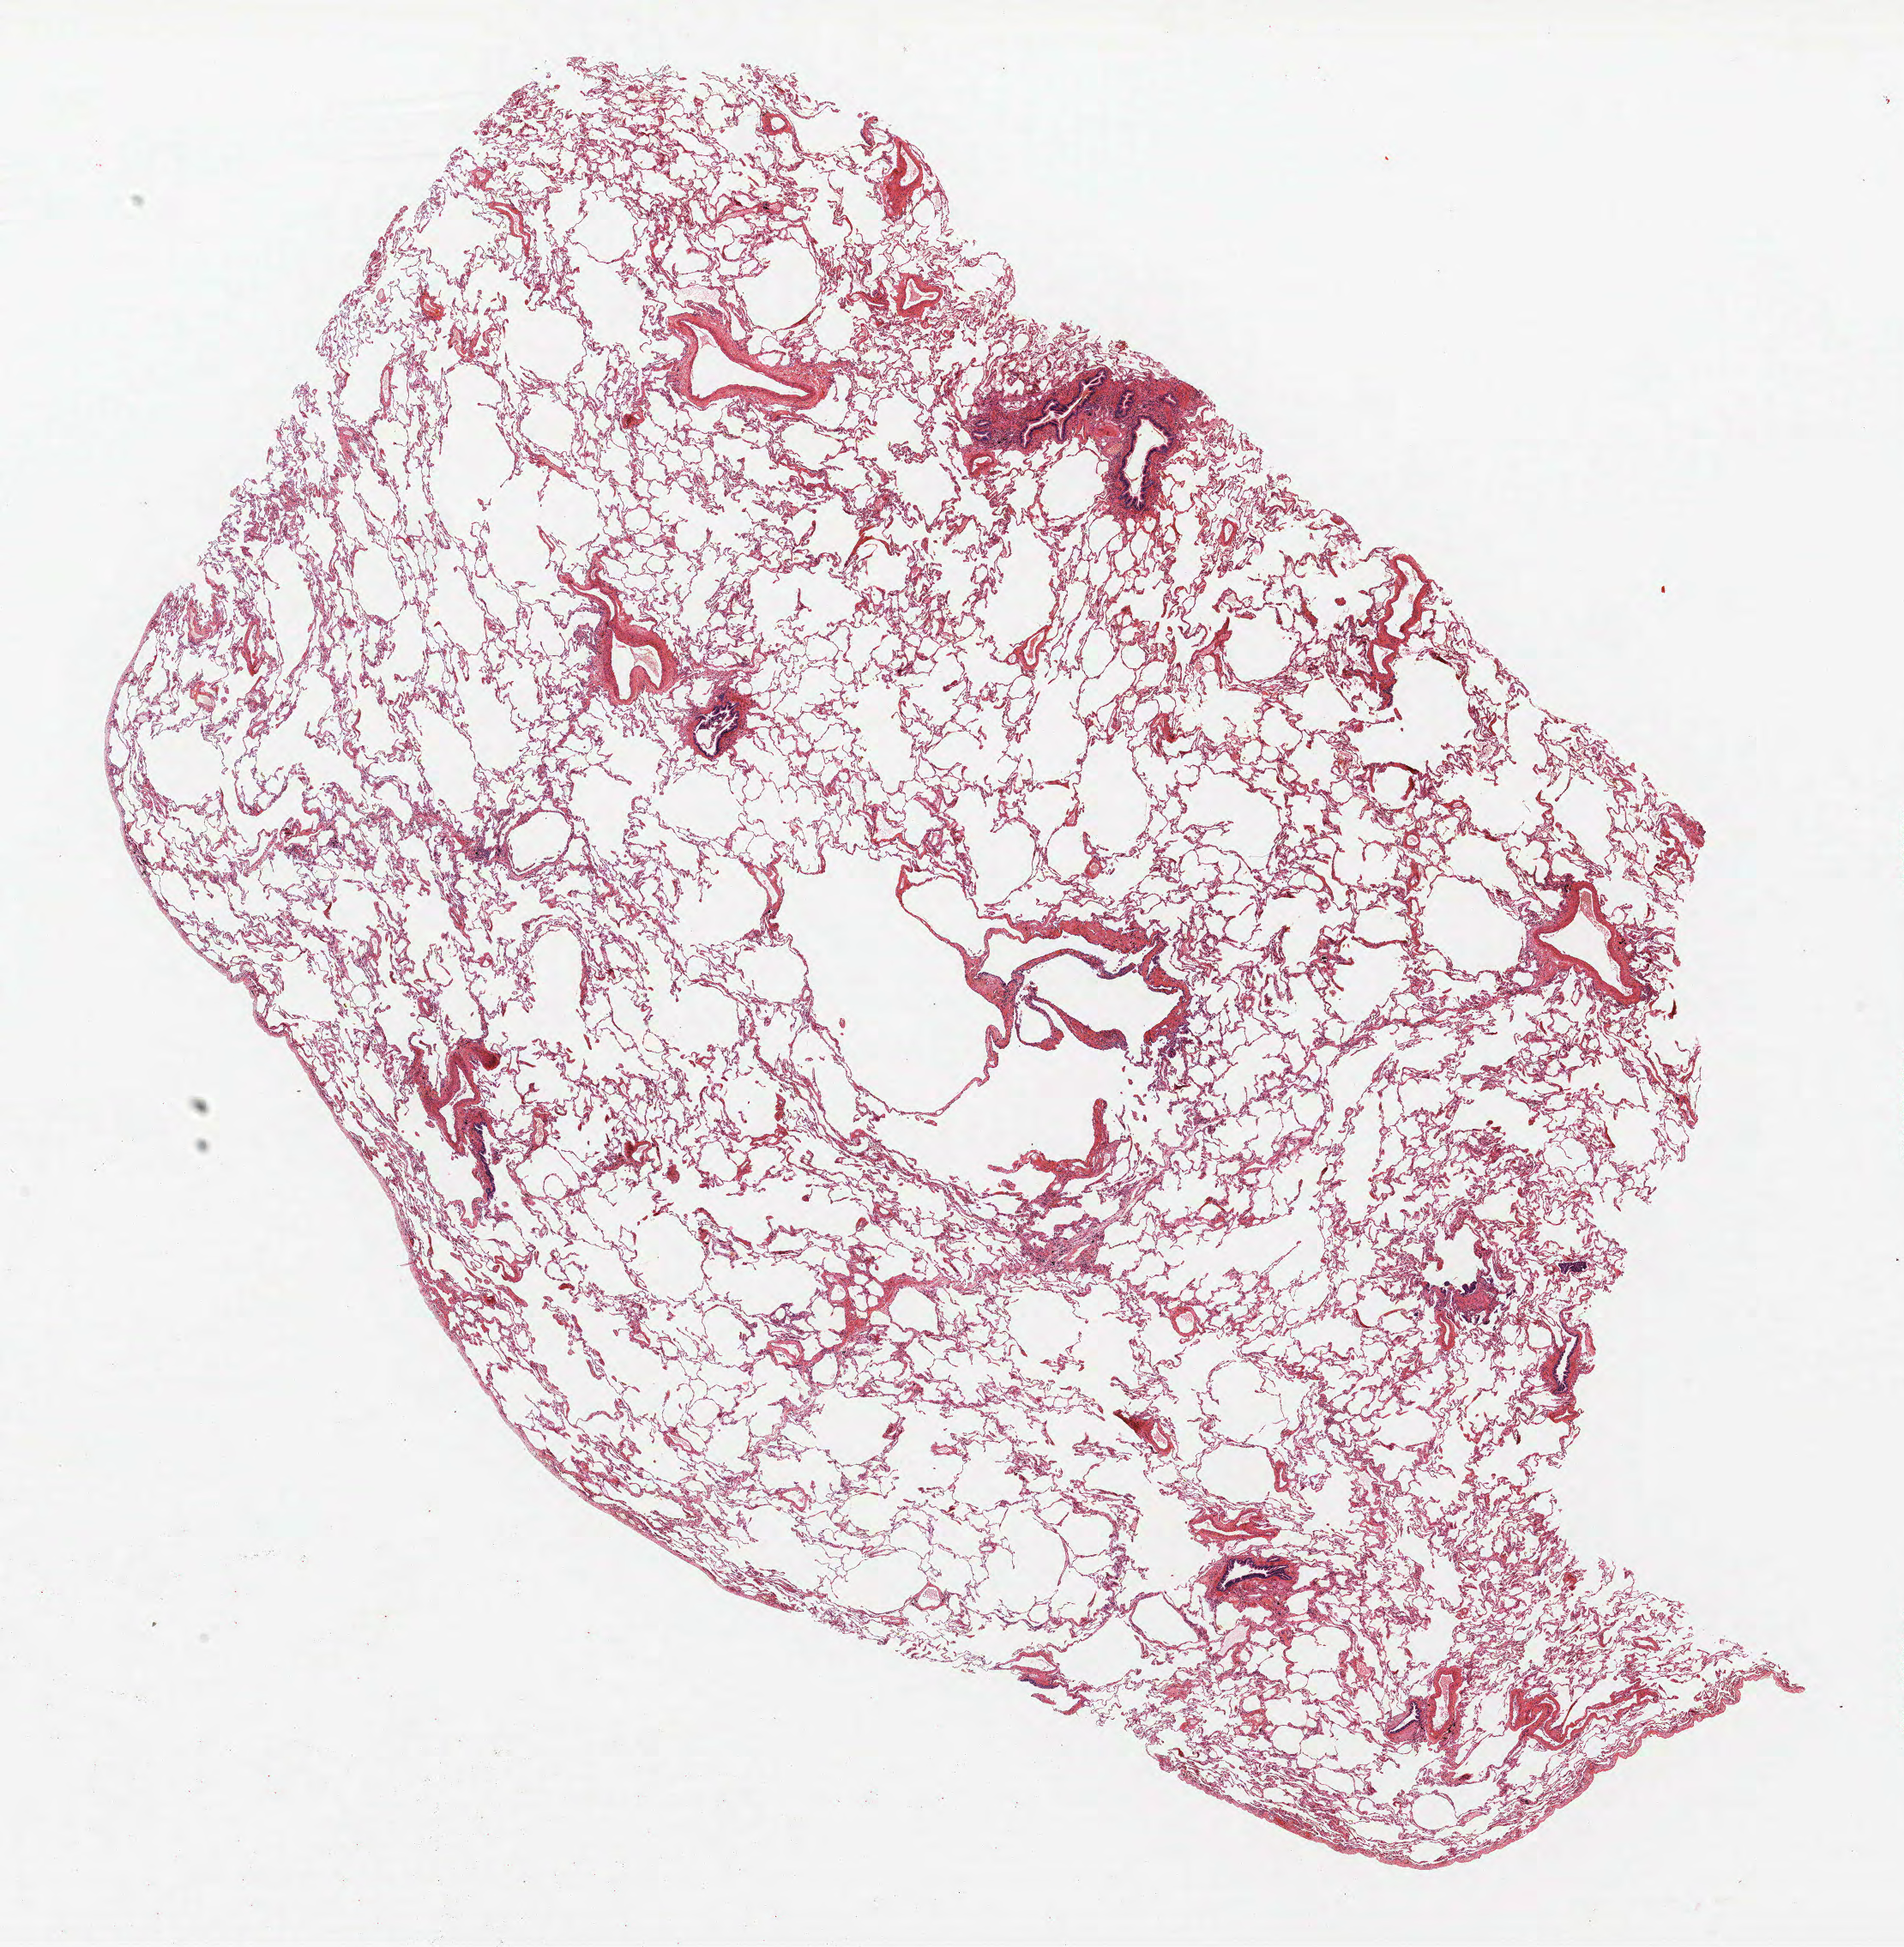
Whole-slide histology image, H&E, a low-resolution overview of the entire scanned area, about 17.8 x 18.2 mm. FFPE section. Lung. Female, age 61 at enrolment. Grade: moderately differentiated (G2).
- tumour size (pathology): 8 mm
- primary tumour location (clinical record): right upper lobe
- ICD-O-3 topography: upper lobe of lung (C34.1)
- stage (AJCC 6th edition): IA
- participant's lung-cancer diagnosis: Adenocarcinoma, NOS